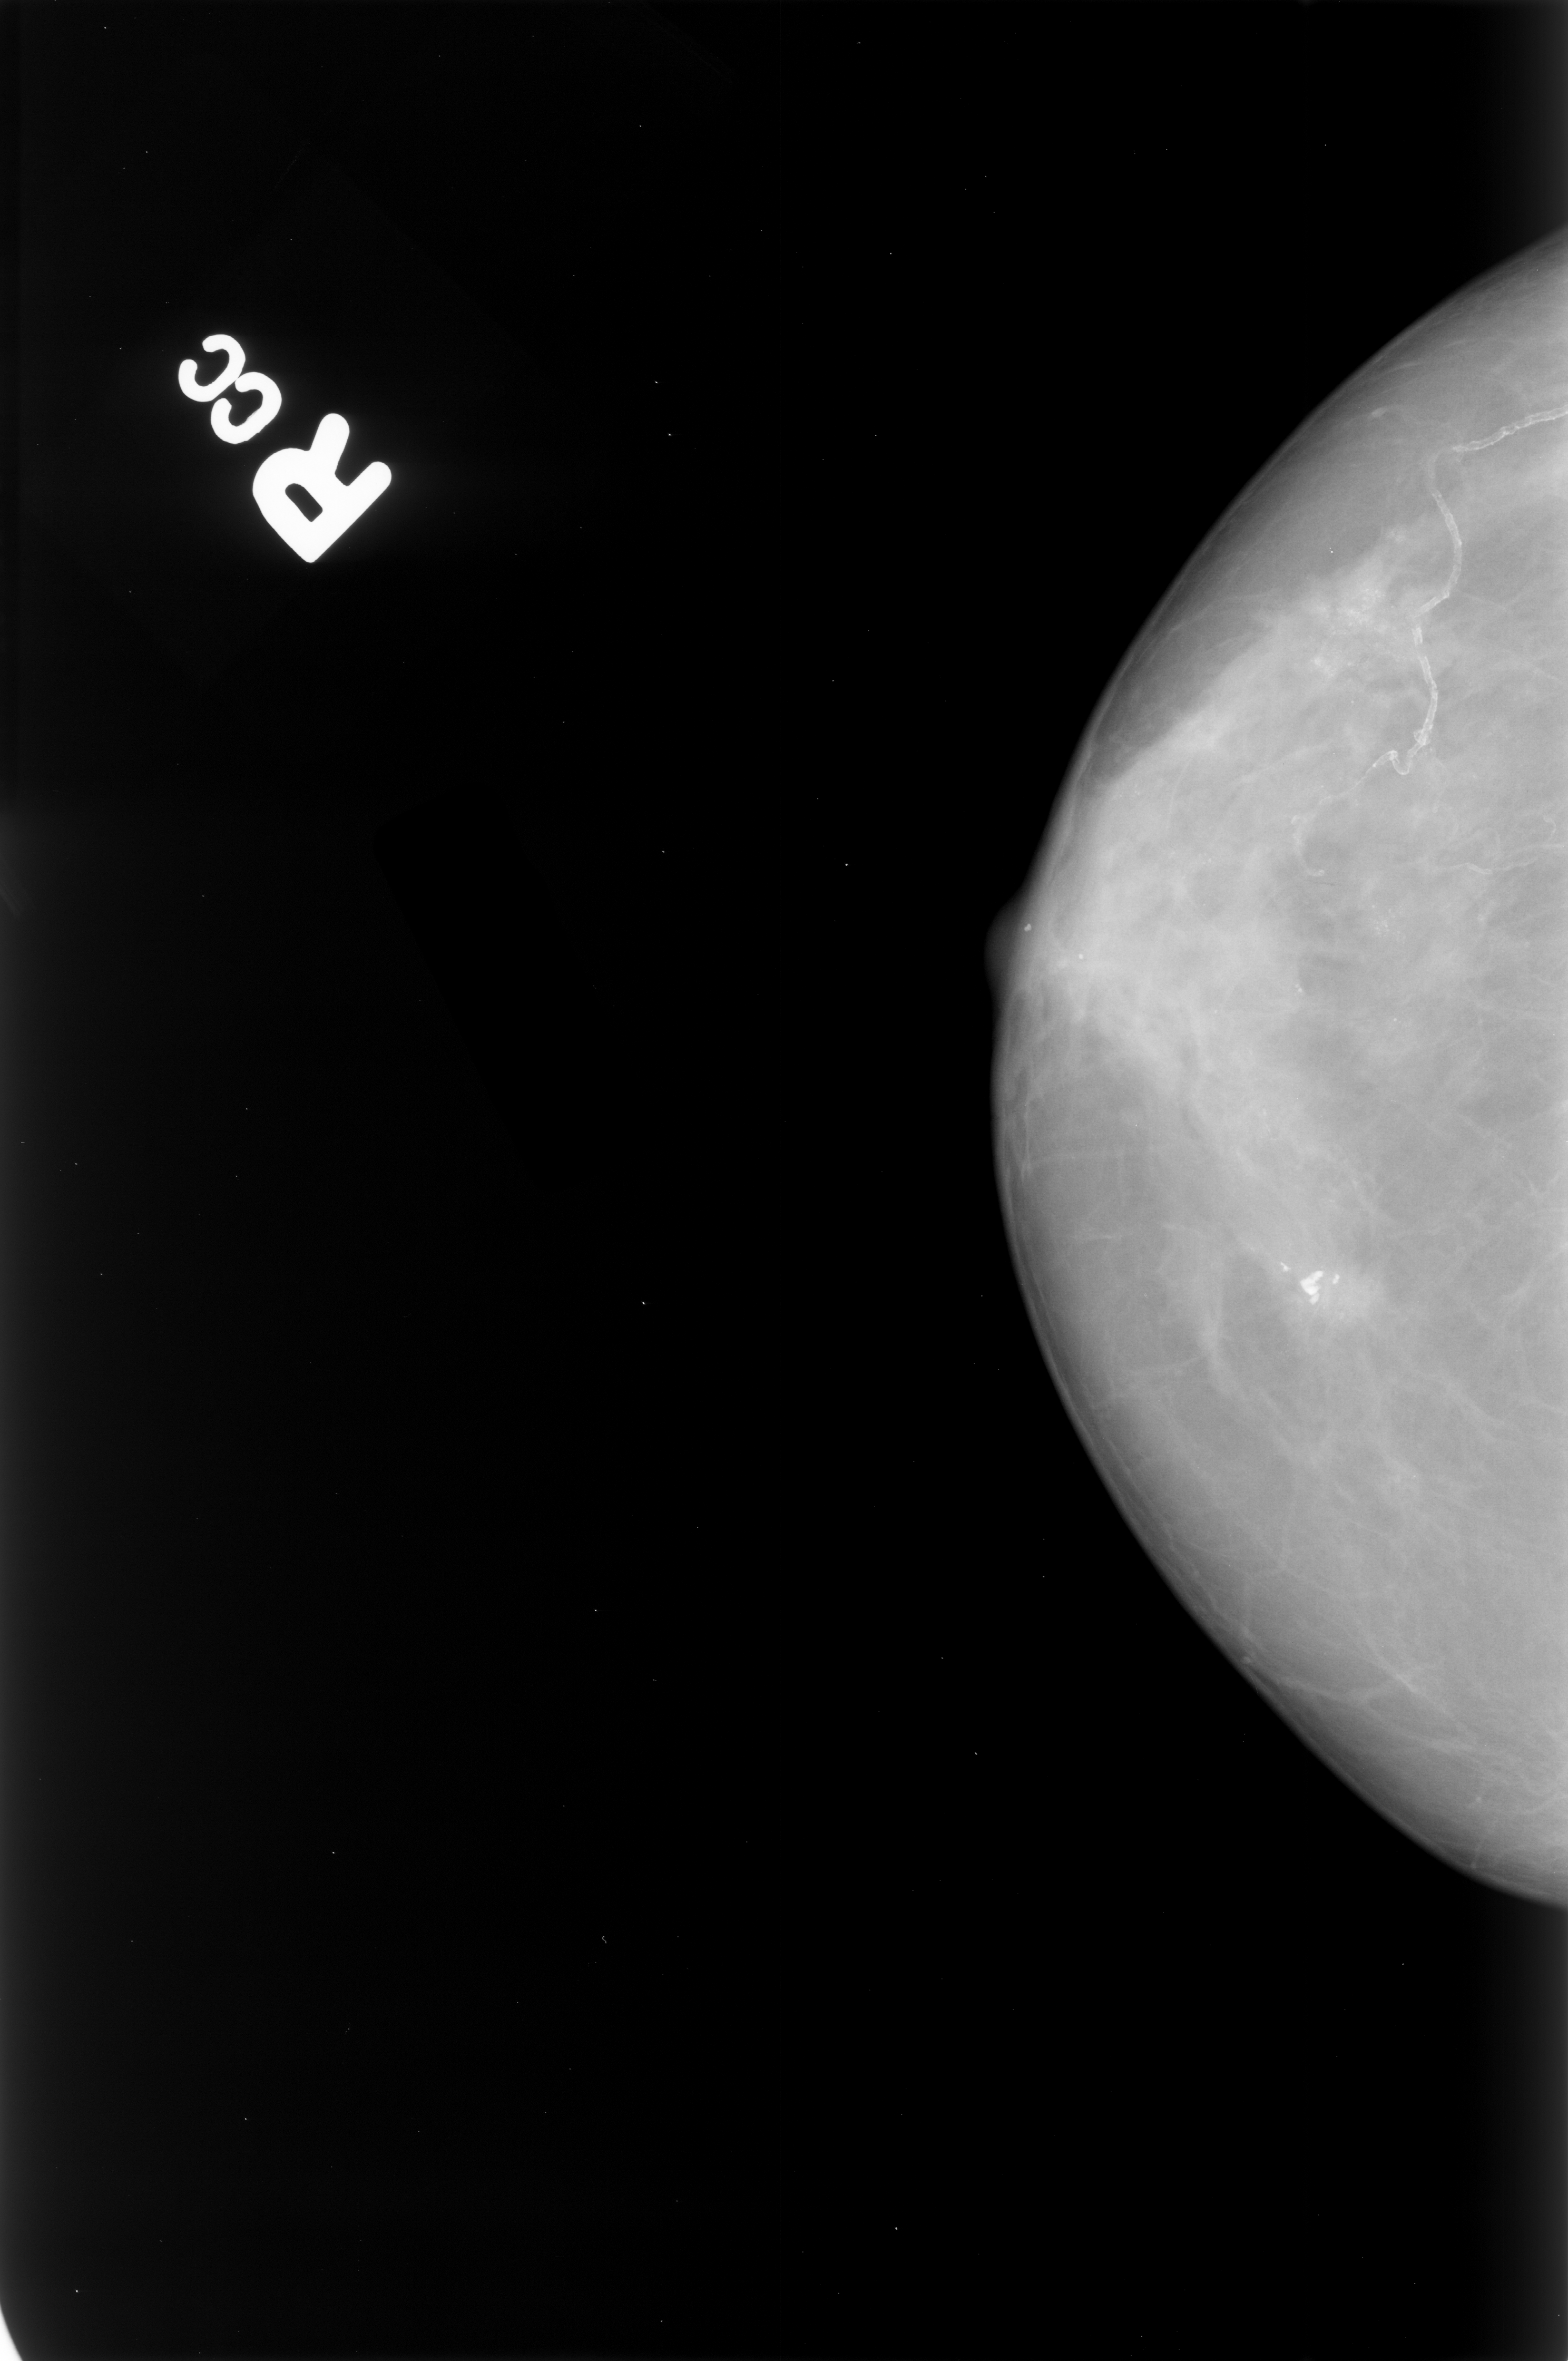
Mammogram (digitized film); right breast; craniocaudal (CC) view; BI-RADS breast density category 3 (scale 1–4).
Abnormality record for this image: calcifications, morphology punctate / pleomorphic, distribution clustered; BI-RADS assessment category 4; pathology (as recorded): malignant.